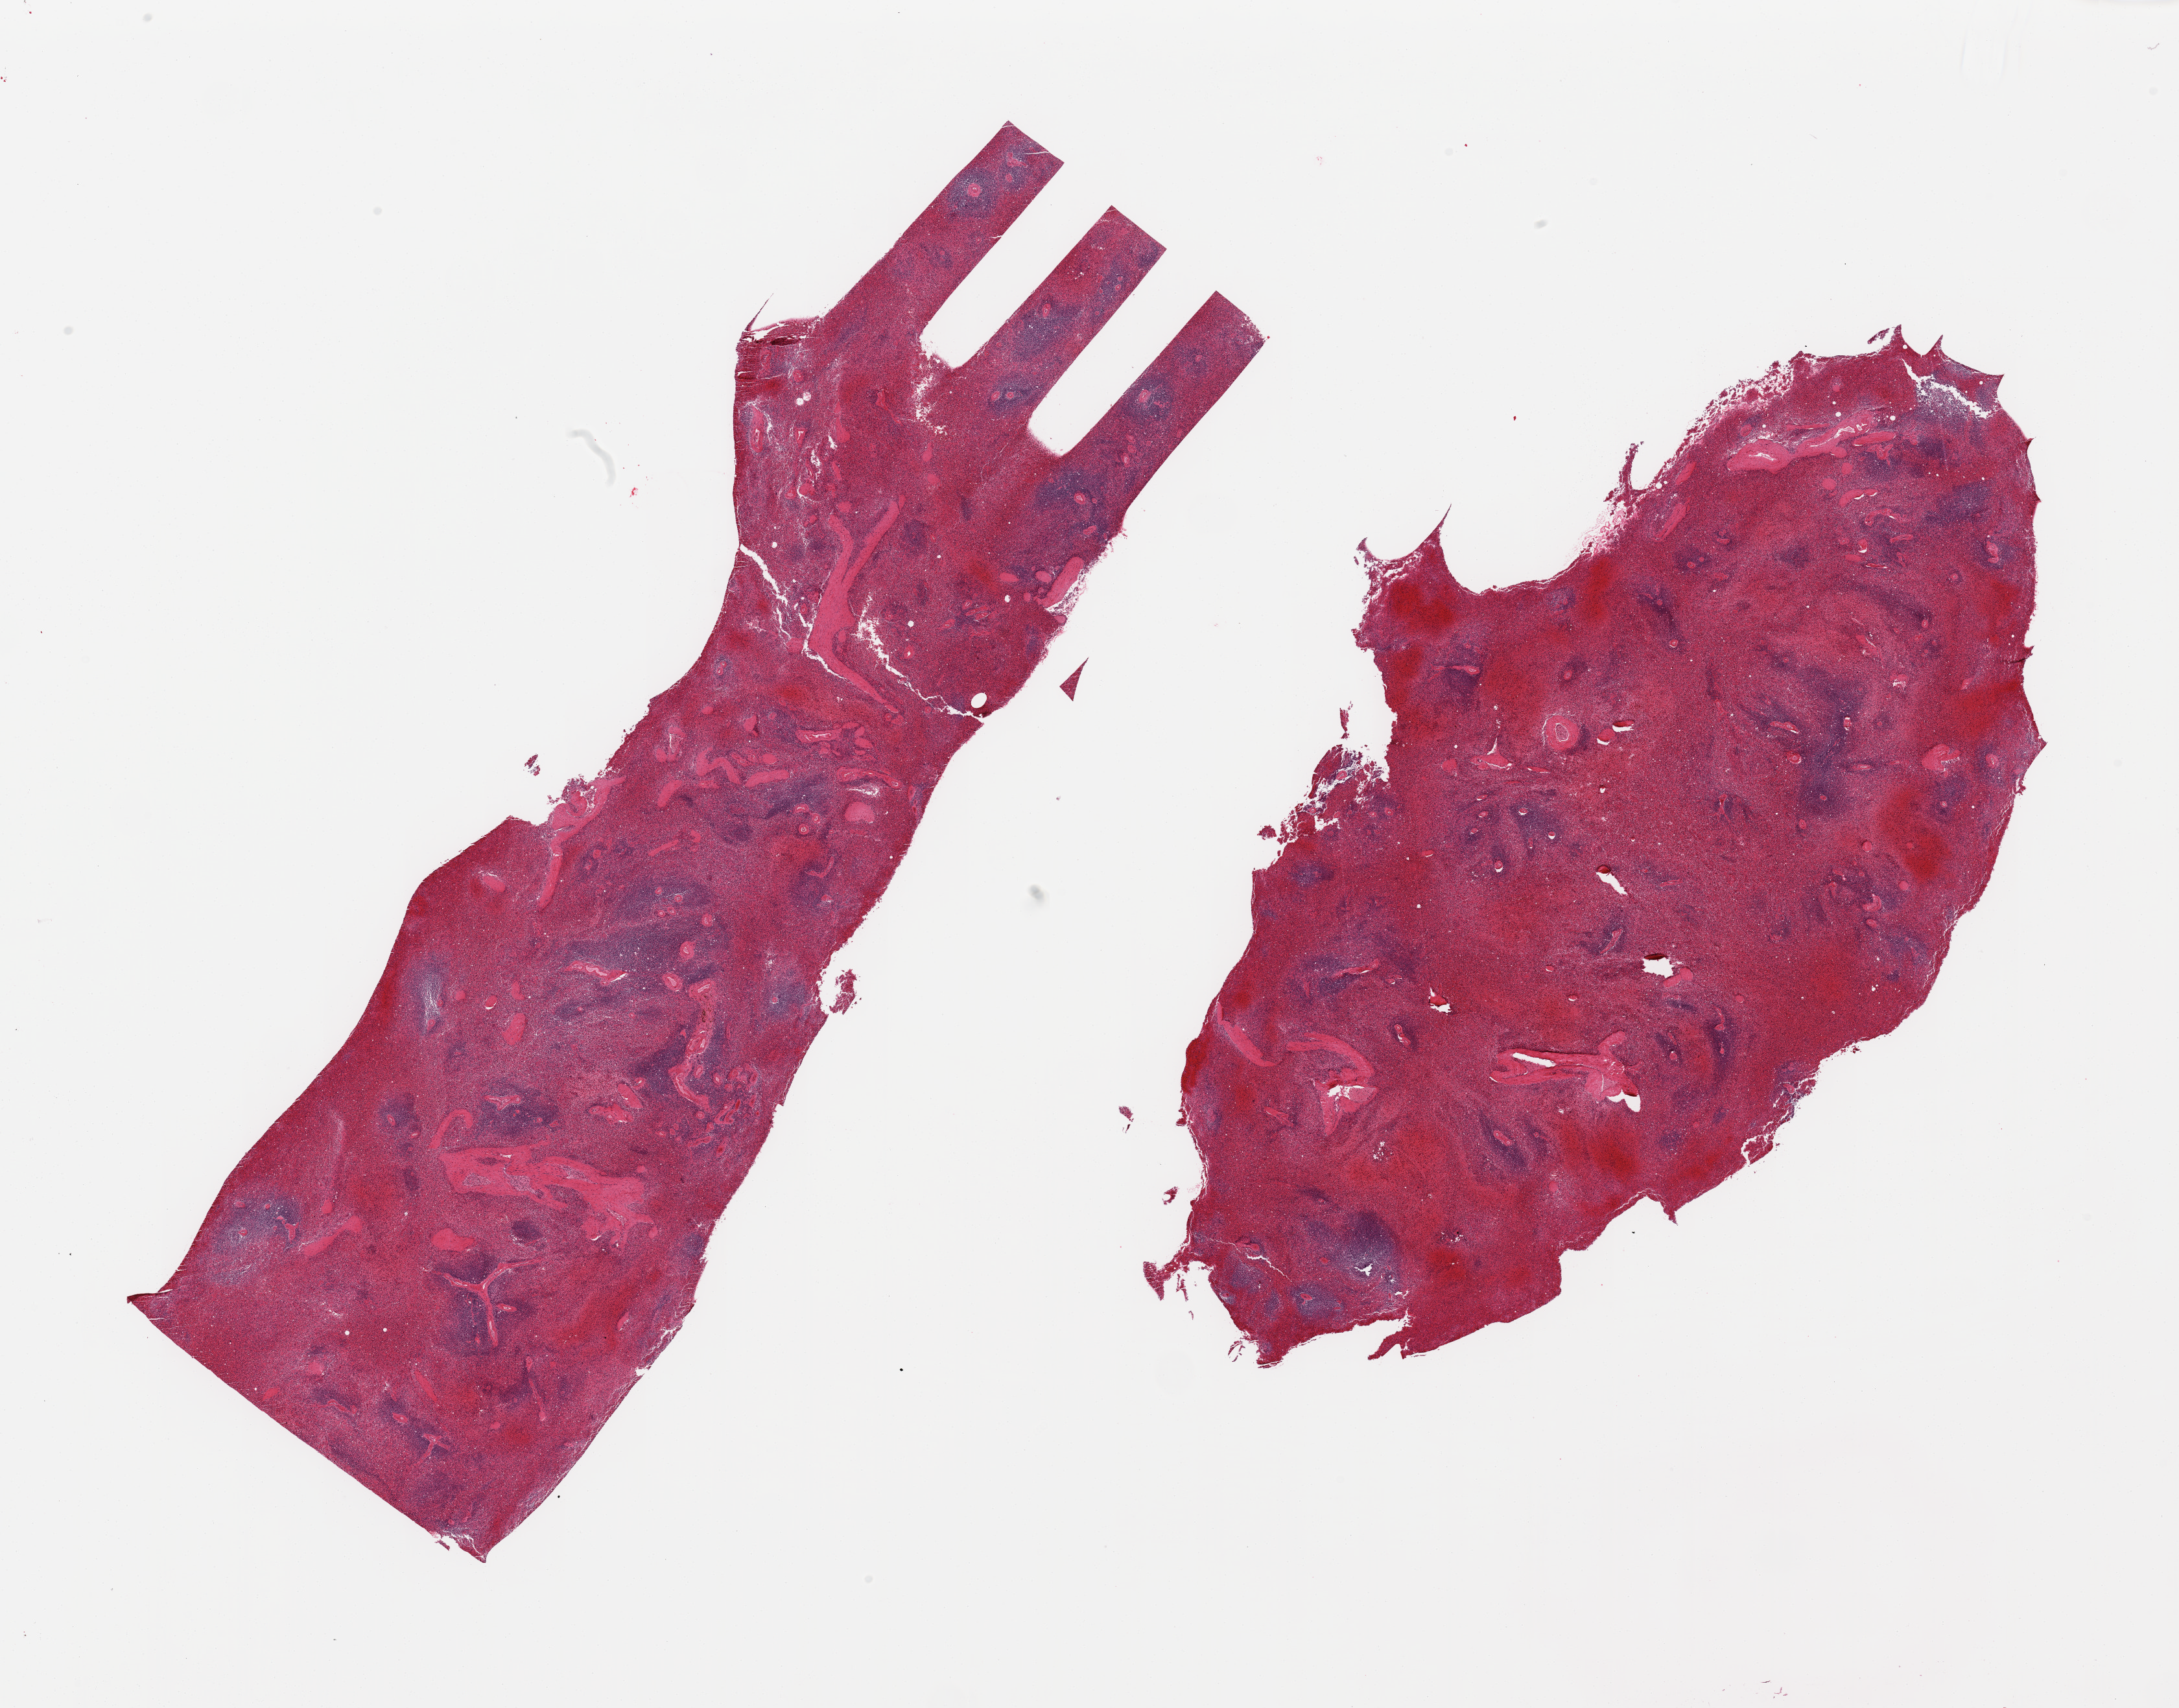
Whole-slide image, haematoxylin and eosin stain, low-resolution overview of the scanned area, about 26.6 x 20.8 mm (slide scanned at 20x). PAXgene-fixed paraffin-embedded (PFPE) section. Sampled site (target tissue): spleen. Tissue donor sample.
• pathologist's review note for this sample: 2 pieces, moderately congested